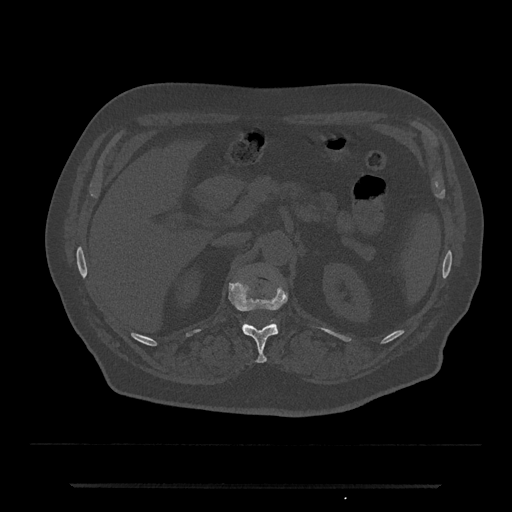
CT including the spine, one axial slice. Position 580 of 797 along the scan axis. Reconstruction kernel Br40s/3. Bone window (W 1800 / L 400 HU). 0.5 mm slice thickness. 512 × 512 image matrix, field of view 434 × 434 mm. Male patient, age 80 years. Case-level facts recorded for this patient, not image findings: primary cancer: prostate; vertebrae with lytic lesions (as recorded): L1, T11.
Outlined on this slice (semi-automatic segmentation, software-assisted and operator-edited):
- L1 vertebra: bounding box [x1, y1, x2, y2] px = [242, 321, 277, 328]
- T12 vertebra: [229, 282, 287, 363]